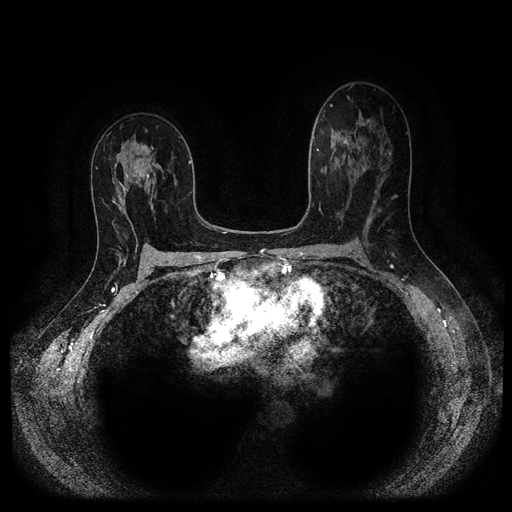
Breast MRI (dynamic contrast-enhanced, multi-phase), one axial slice. Dynamic contrast-enhanced series, time point 2 of 5 at this slice position (early post-contrast). 1.5 T. TE 2.6 ms, TR 5.3 ms. 2.2 mm slice thickness. 512 × 512 image matrix, field of view 340 × 340 mm. Patient: female, 50 years.
Outlined on this slice (semi-automatic segmentation, software-assisted and operator-edited):
- breast lesion (labelled 'tumour' in the annotation; benign lesions carry a separate 'benign' label): bounding box (x1, y1, x2, y2) in pixels: (129, 143, 157, 179)